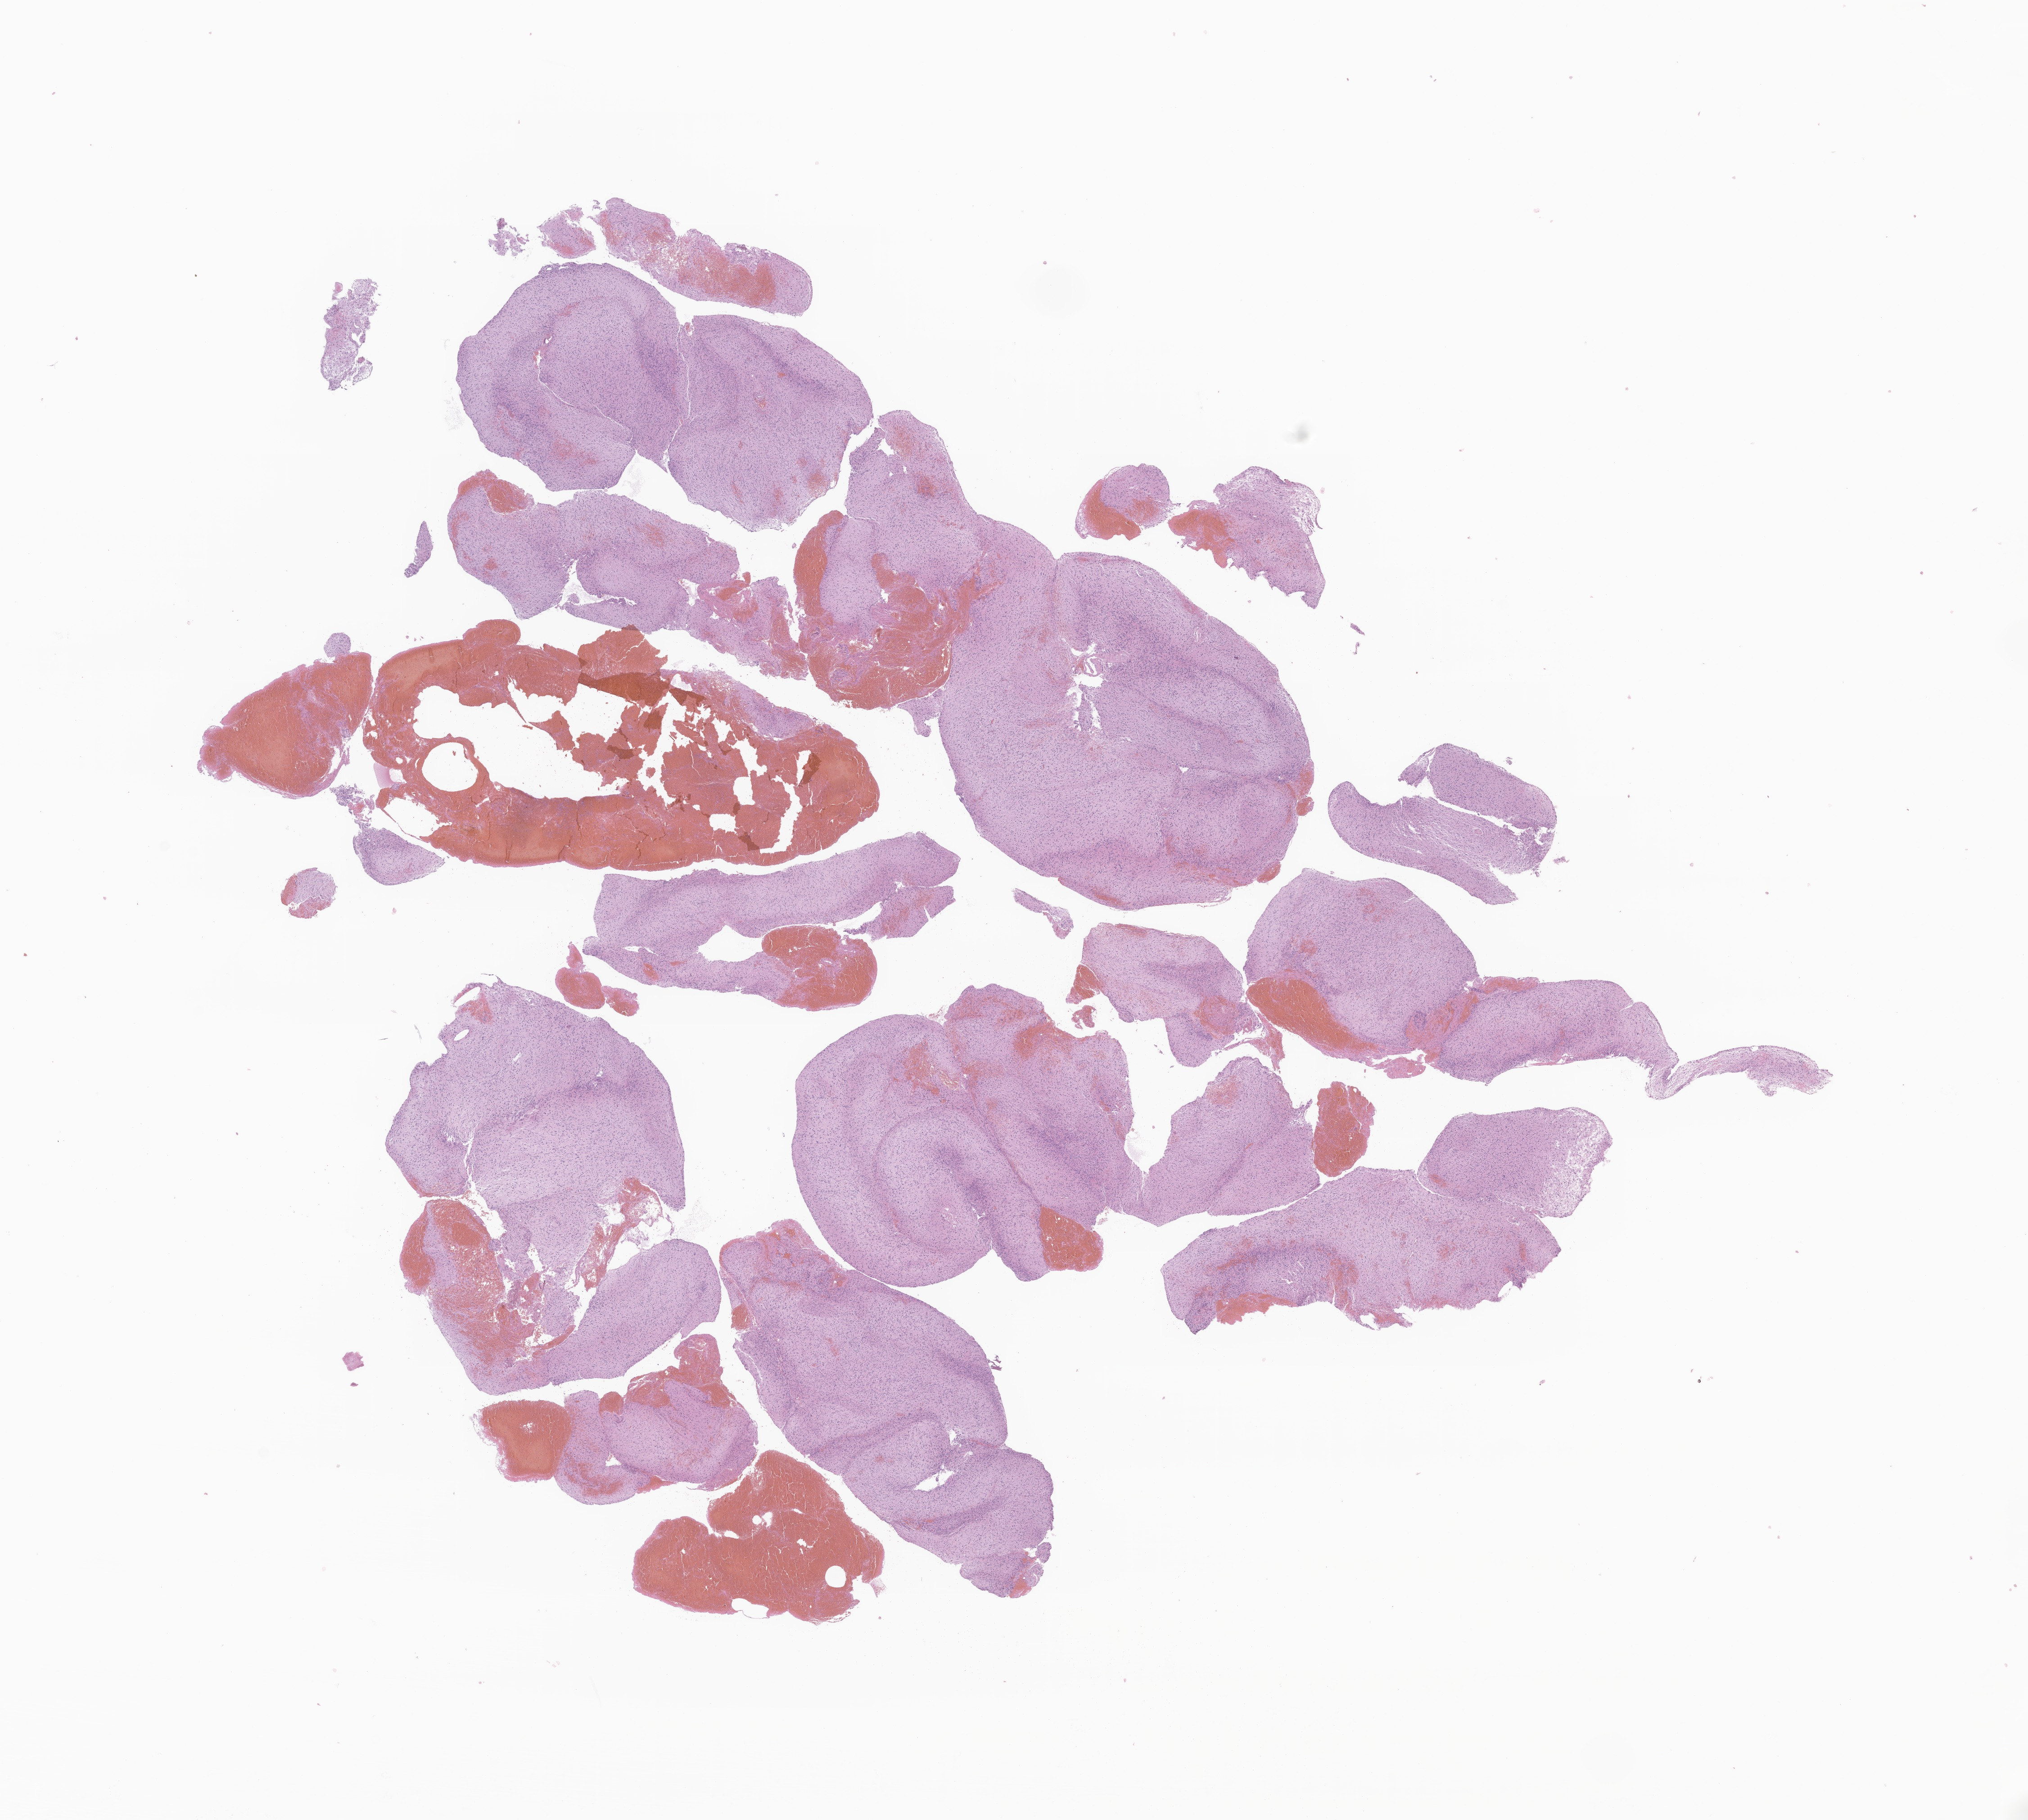
Digitized hematoxylin and eosin (H&E)-stained section of tumor tissue from the brain, shown as a low-resolution overview of the whole scanned area (about 19.0 x 17.0 mm). FFPE section. Female patient, age 167 months (13 years 11 months).
Diagnosis: Glioma, malignant.